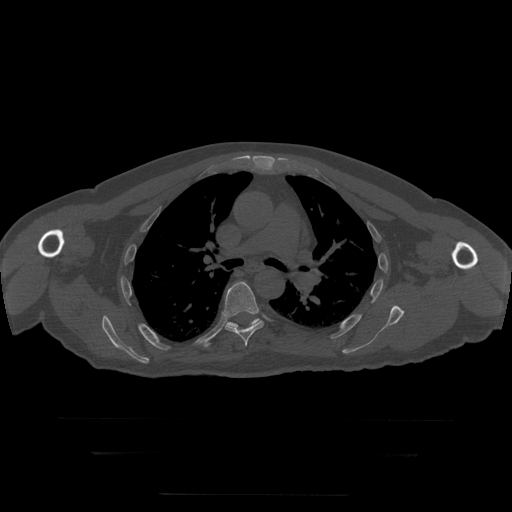
CT including the spine, one axial slice. 120 kVp. Bone window (W 1800 / L 400 HU). 1.25 mm slice thickness. 512 × 512 image matrix, field of view 510 × 510 mm. Patient age 73 years. From the clinical record (not read from this slice): primary cancer: prostate.
Annotated regions visible in this slice (semi-automatic segmentation, software-assisted and operator-edited):
- T6 vertebra: bounding box (x1, y1, x2, y2) in pixels: (224, 282, 265, 347)
- T7 vertebra: (227, 319, 261, 328)